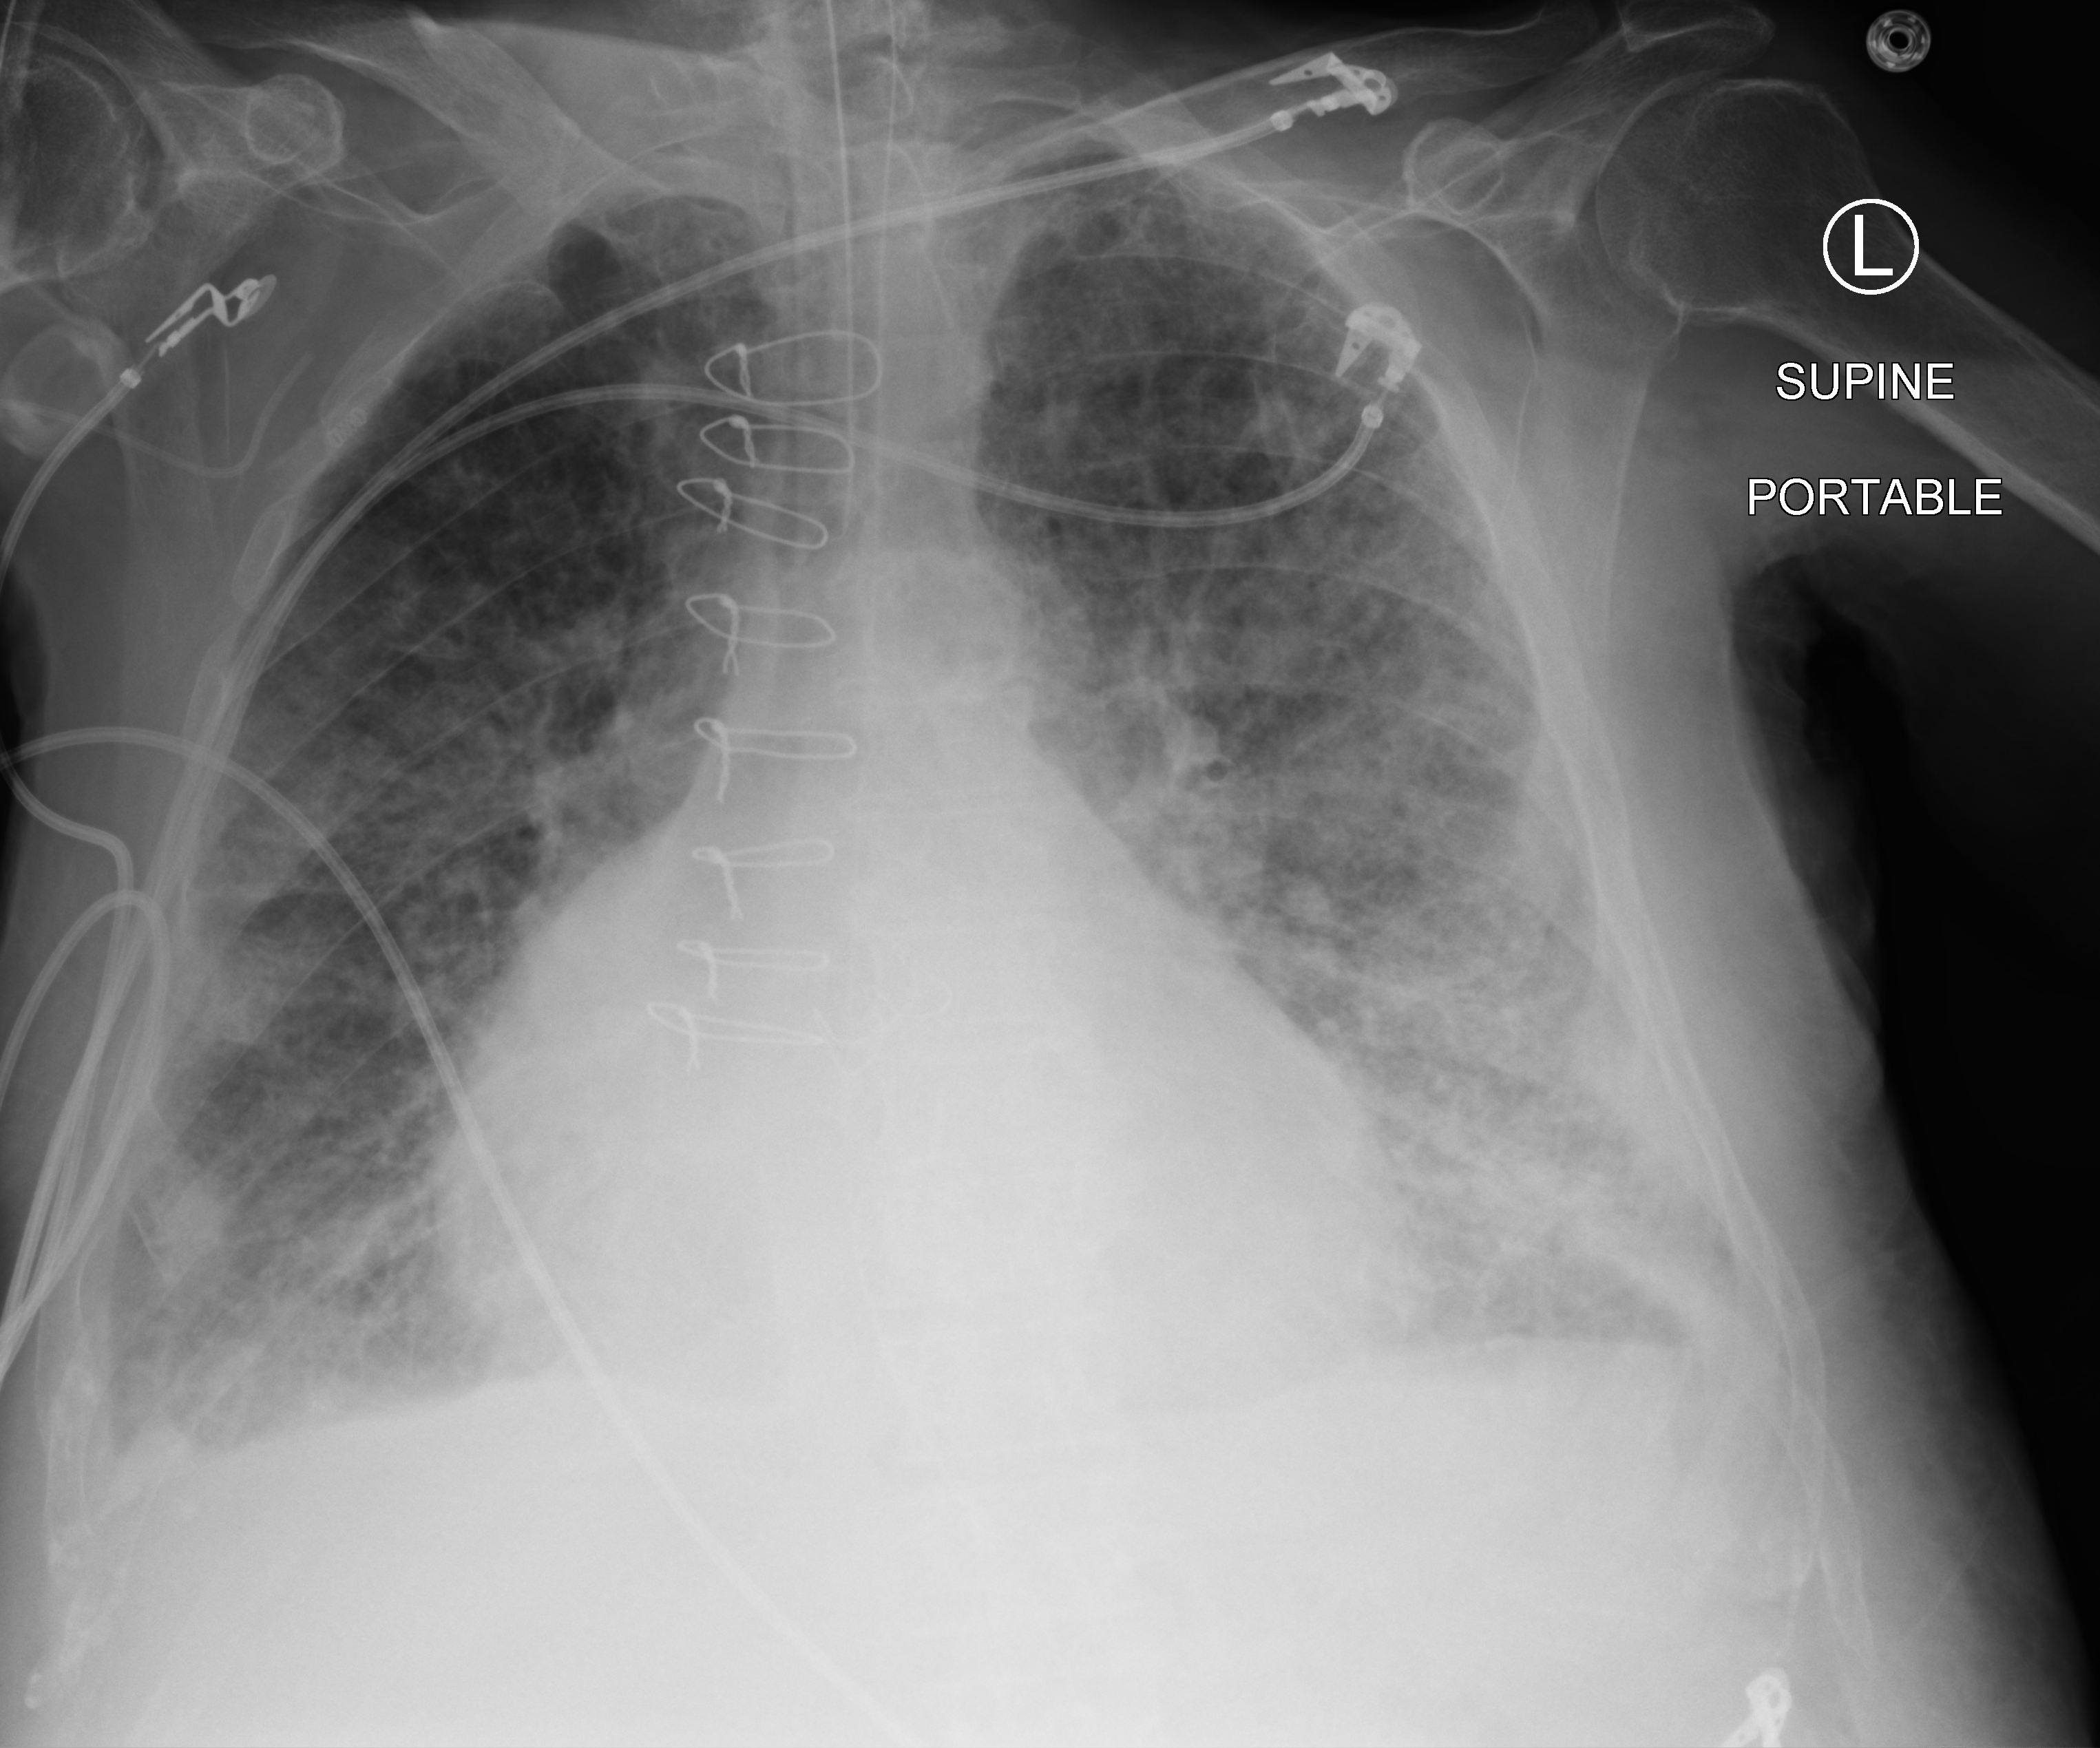
Chest X-ray (portable), anteroposterior (AP) projection. Male patient hospitalised with COVID-19, age 75–90 years.
From the hospital-stay record, not from the radiograph (when in the stay this image was taken is not recorded): admitted to intensive care during this hospital stay: yes; mechanically ventilated during this hospital stay: yes.